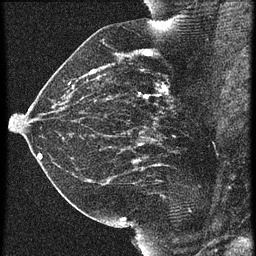
Breast MRI (dynamic contrast-enhanced), one sagittal slice. Slice 29 of 60 in the series (ordered by position). 3 images stored at this slice position (order not interpretable as contrast timing). 1.5 T. TE 4.2 ms, TR 21.3 ms. 1.5 mm slice thickness. 256 × 256 image matrix, field of view 180 × 180 mm. Patient: female, 42 years. From the clinical record (not read from this slice): setting: breast cancer imaged before/during neoadjuvant chemotherapy; receptor status: HER2-positive.
Structures marked on this image (semi-automatic segmentation, software-assisted and operator-edited):
- analysis volume of interest (the breast-tissue region the enhancement analysis was run in; not a lesion): box from (x=122, y=82) to (x=195, y=147) px
- tumour enhancement mask (voxels above the 90 % enhancement threshold inside the analysis volume of interest): (x=144, y=84)–(x=168, y=99)